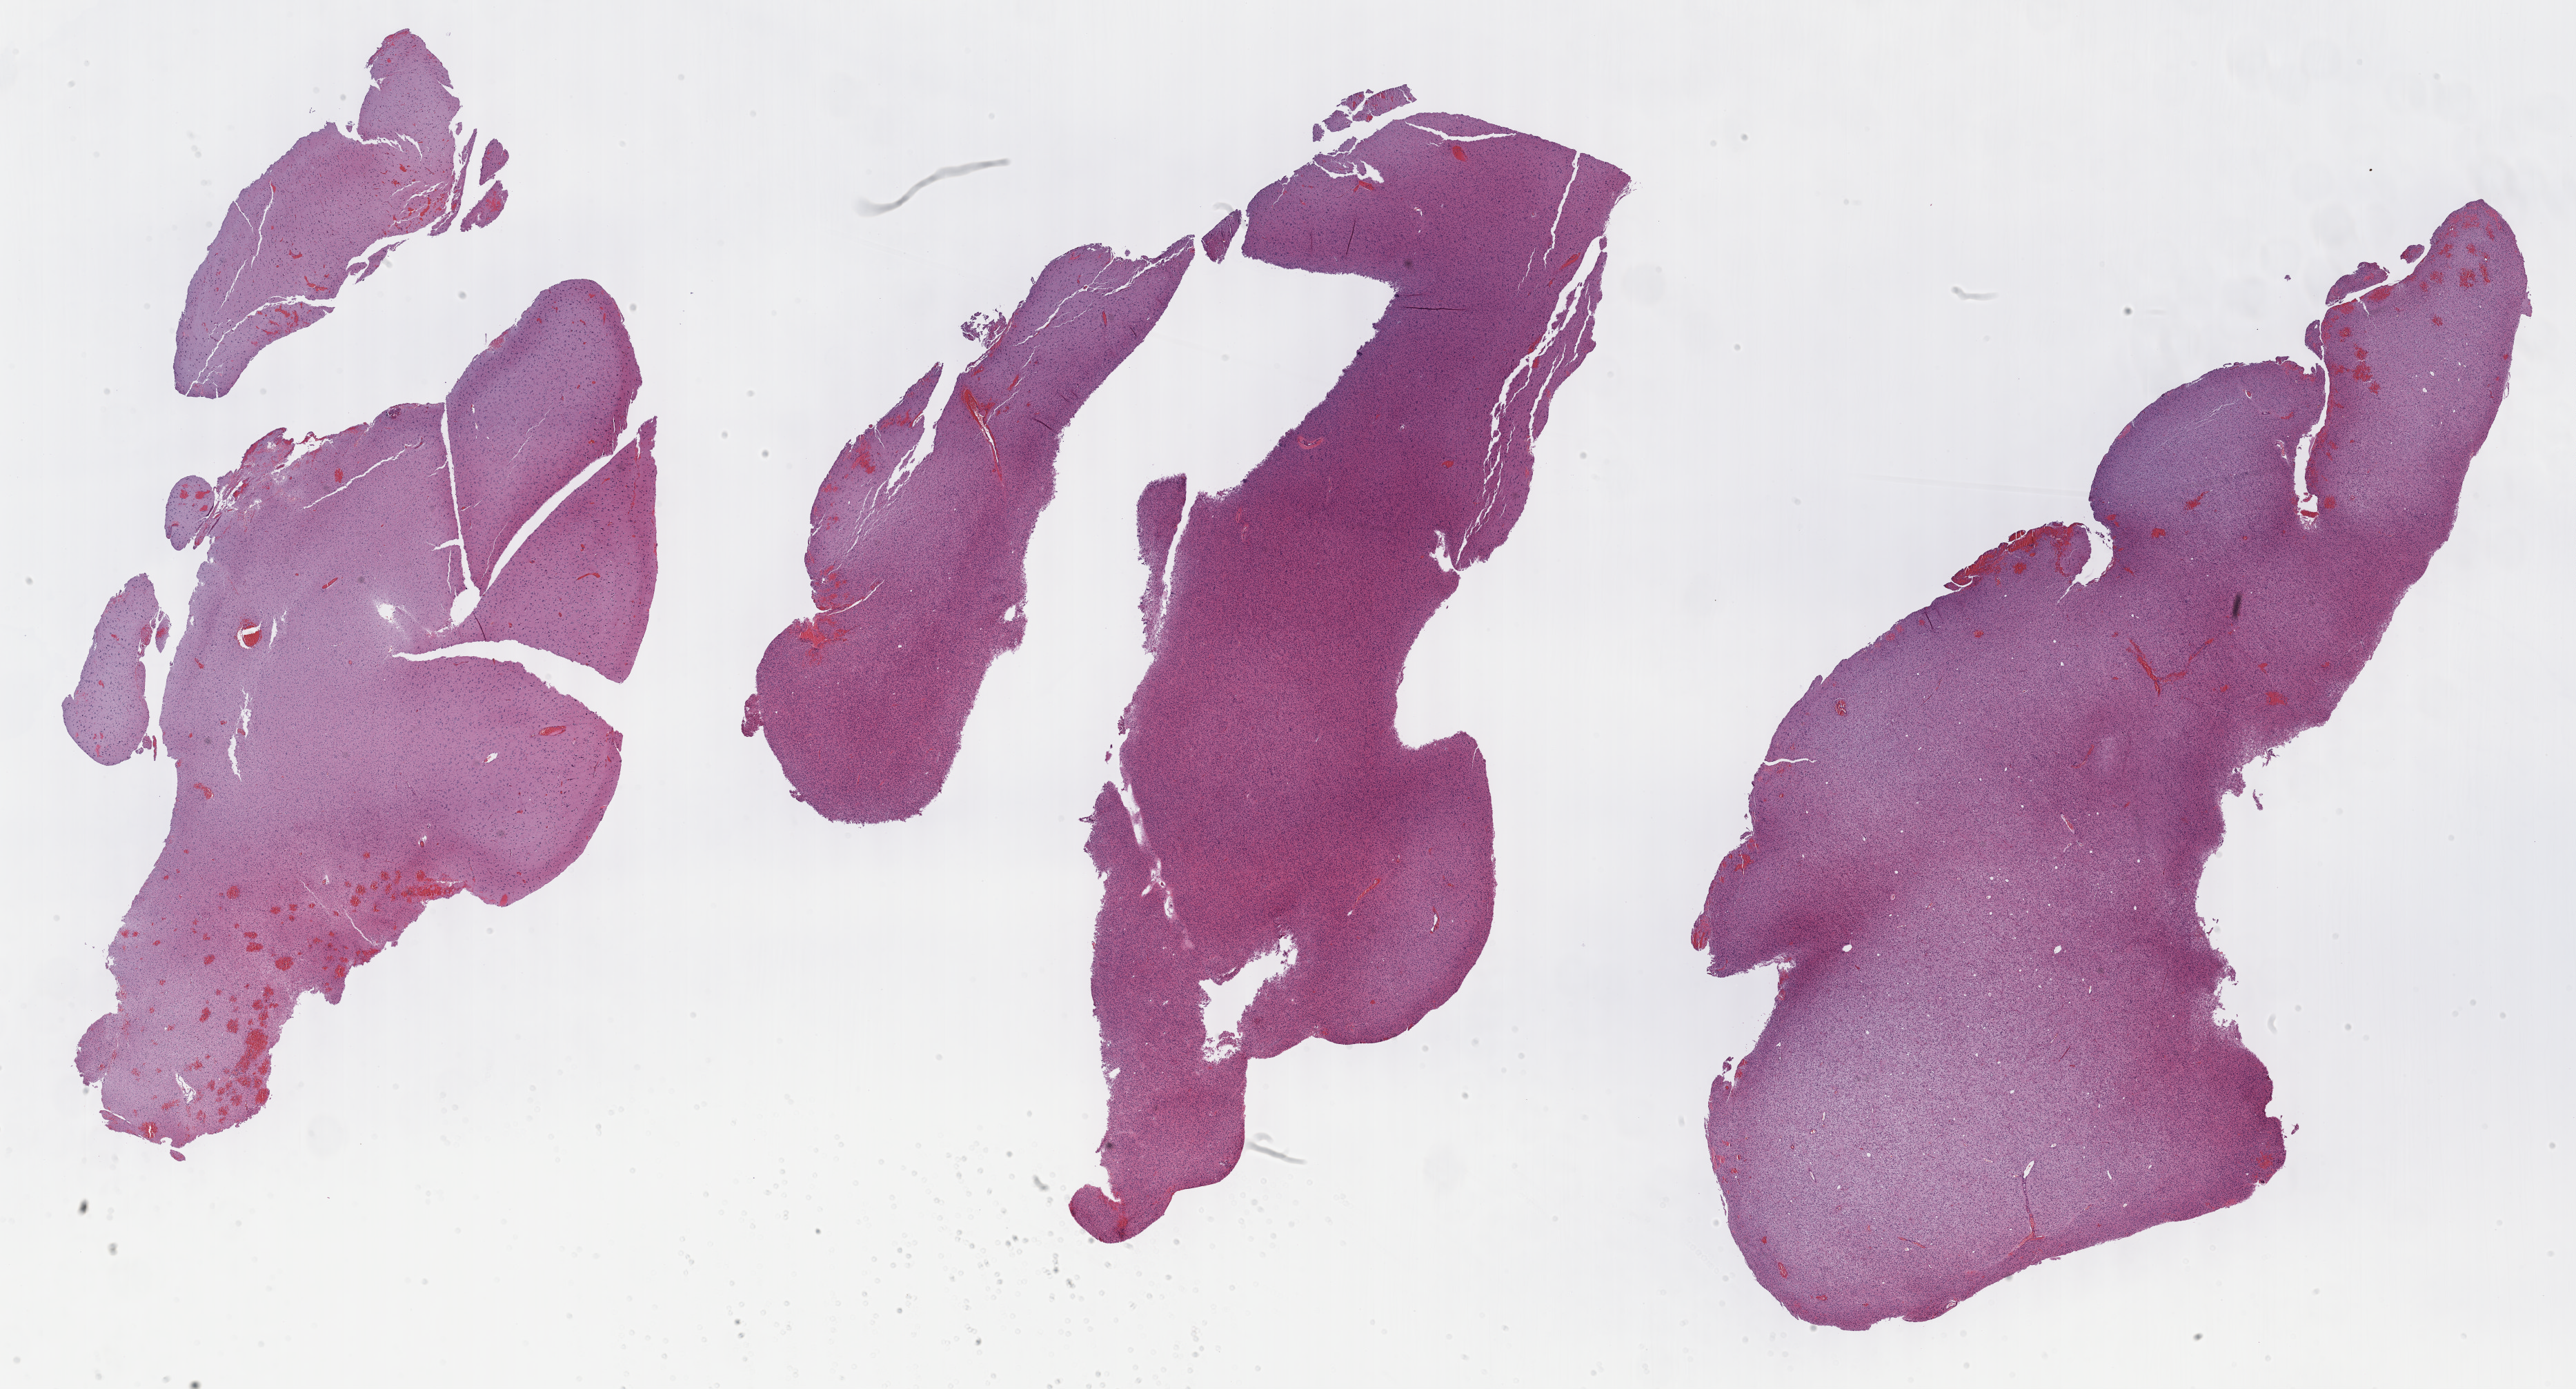
Digitized H&E-stained tissue section (whole slide) — shown as a low-resolution overview of the whole scanned area (about 30.2 x 16.3 mm, acquisition: 40x scan). Formalin-fixed paraffin-embedded (FFPE) diagnostic section. Sample: primary tumour, brain. Male, age 25 years at initial diagnosis. Histologic grade: G2 (moderately differentiated).
• histologic diagnosis: Oligodendroglioma, NOS (cerebrum)